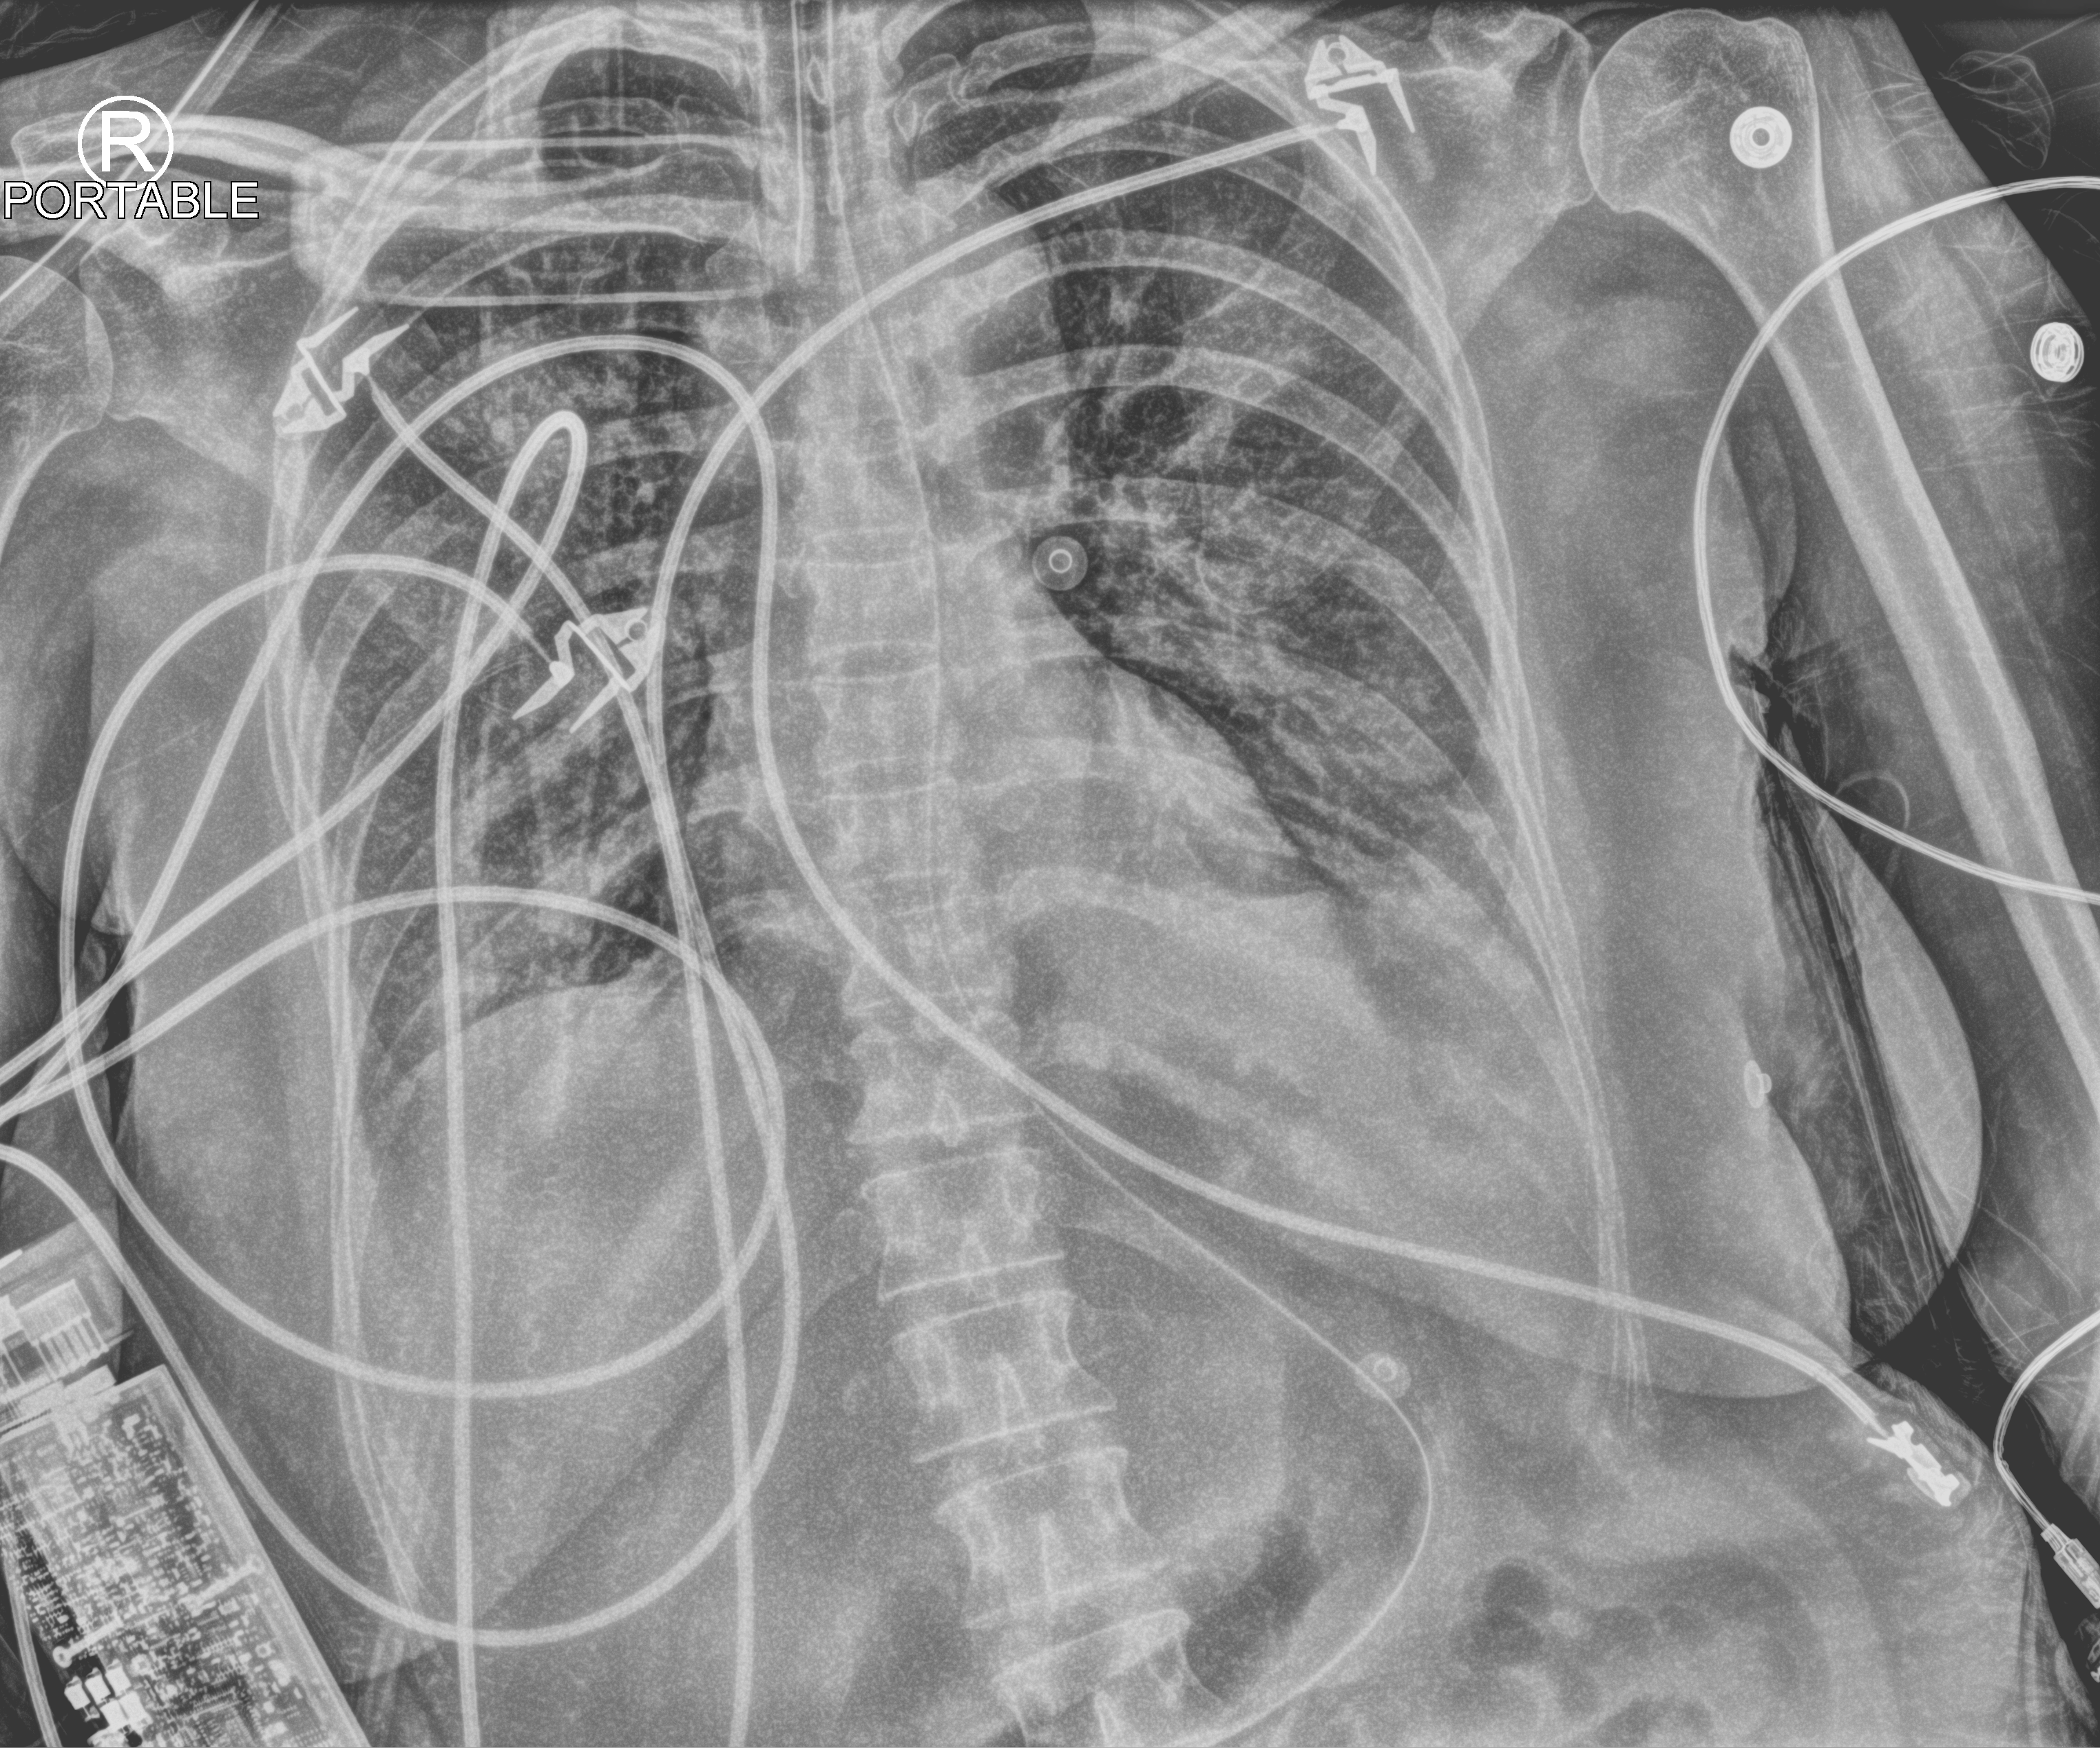
Chest X-ray (portable), anteroposterior (AP) projection. Patient hospitalised with COVID-19; female, aged 18–59 years.
Admission-level facts for this patient (not findings on this image; timing relative to this image not recorded):
- admitted to intensive care during this hospital stay: yes